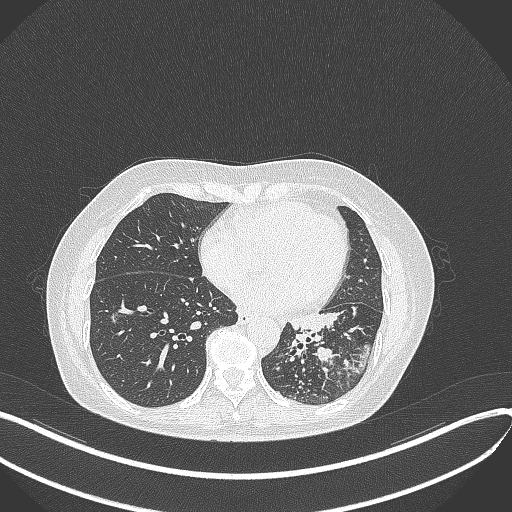
Chest CT, one axial slice; slice 154 of 429 in the series (ordered by position); reconstruction kernel B70f; 100 kVp; lung window (W 1500 / L -600 HU); 1 mm slice thickness; 512 × 512 image matrix. Female patient, age 63 years. From the clinical record (not read from this slice): clinical TNM (as recorded): T1b N0 M0; histopathological grade: G2-3.
Structures marked on this image (rectangle marked by the reading radiologist):
- lung tumour (recorded histology: adenocarcinoma): box from (x=285, y=305) to (x=344, y=342) px